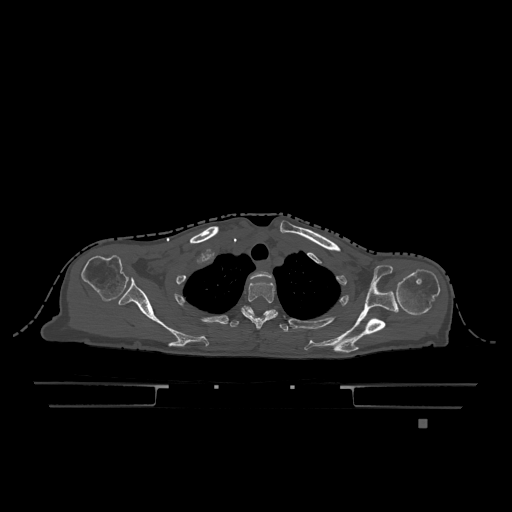
CT including the spine, one axial slice; position 955 of 1317 along the scan axis; bone window (W 1800 / L 400 HU); 0.5 mm slice thickness; 512 × 512 image matrix. Female patient, age 74 years. Case-level facts recorded for this patient, not image findings: primary cancer: lung.
Structures marked on this image (semi-automatically segmented with operator editing):
- T1 vertebra: bounding box (x1, y1, x2, y2) in pixels: (250, 271, 272, 279)
- T2 vertebra: (241, 281, 278, 329)
- T3 vertebra: (230, 308, 288, 332)
- T6 vertebra: (243, 306, 276, 317)